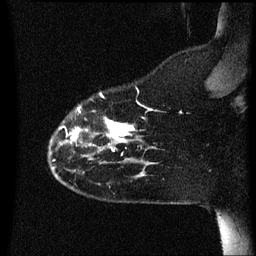
Breast MRI (dynamic contrast-enhanced), one sagittal slice; position 11 of 60 along the scan axis; dynamic contrast-enhanced series, image 2 of 3 at this slice position (ordered by acquisition); 1.5 T; TE 4.2 ms, TR 8.4 ms; 256 × 256 image matrix, field of view 200 × 200 mm. Female patient, age 35 years. From the clinical record (not read from this slice): setting: breast cancer imaged before/during neoadjuvant chemotherapy; receptor status: HER2-positive.
Structures marked on this image (semi-automatic segmentation, software-assisted and operator-edited):
- analysis volume of interest (the breast-tissue region the enhancement analysis was run in; not a lesion): box from (x=49, y=90) to (x=159, y=173) px
- tumour enhancement mask (voxels above the 70 % enhancement threshold inside the analysis volume of interest): (x=59, y=94)–(x=146, y=151)